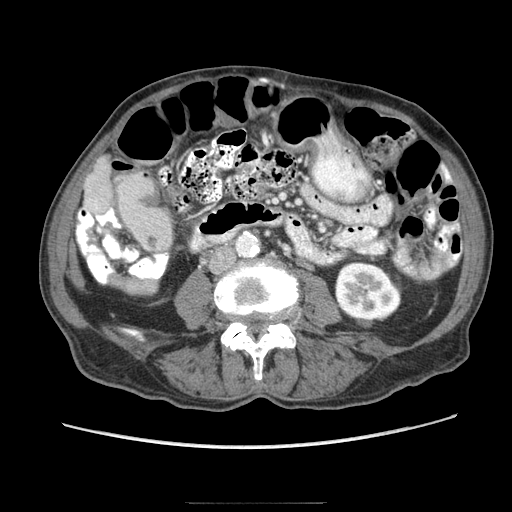
Contrast-enhanced abdominal CT (liver protocol), one axial slice; slice 10 of 83 in the series (ordered by position); soft-tissue window (W 400 / L 40 HU); 2.5 mm slice thickness; 512 × 512 image matrix, field of view 360 × 360 mm. Case-level facts recorded for this patient, not image findings: diagnosis: hepatocellular carcinoma (patient treated with transarterial chemoembolisation; whether this scan precedes or follows treatment is not stated here); TNM stage (as recorded): Stage-I; Child-Pugh class: A; tumour nodularity: uninodular.
Structures marked on this image (semi-automatic segmentation, software-assisted and operator-edited):
- liver parenchyma outside the tumour (the mass and vessels are separate outlines, so this box may not span the whole liver): box from (x=82, y=156) to (x=112, y=214) px
- liver vessels: (x=94, y=201)–(x=98, y=210)